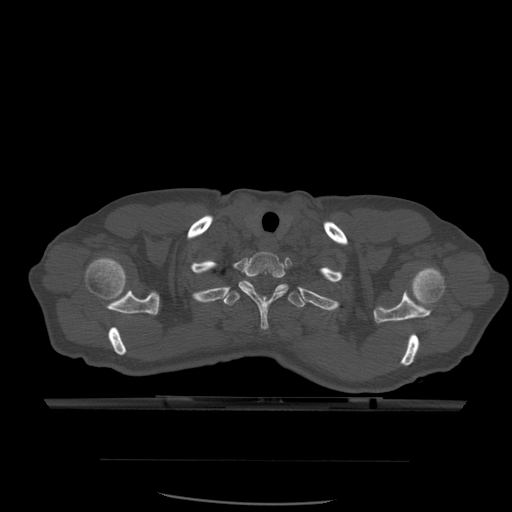
CT including the spine, one axial slice. Slice 466 of 574 in the series (ordered by position). Bone window (W 1800 / L 400 HU). 1.25 mm slice thickness. 512 × 512 image matrix. Patient age 48 years. Case-level facts recorded for this patient, not image findings: primary cancer: lung; vertebrae with lytic lesions (as recorded): T11.
Outlined on this slice (semi-automatically segmented with operator editing):
- T1 vertebra: bounding box (x1, y1, x2, y2) in pixels: (239, 252, 288, 330)
- T2 vertebra: (221, 280, 306, 308)